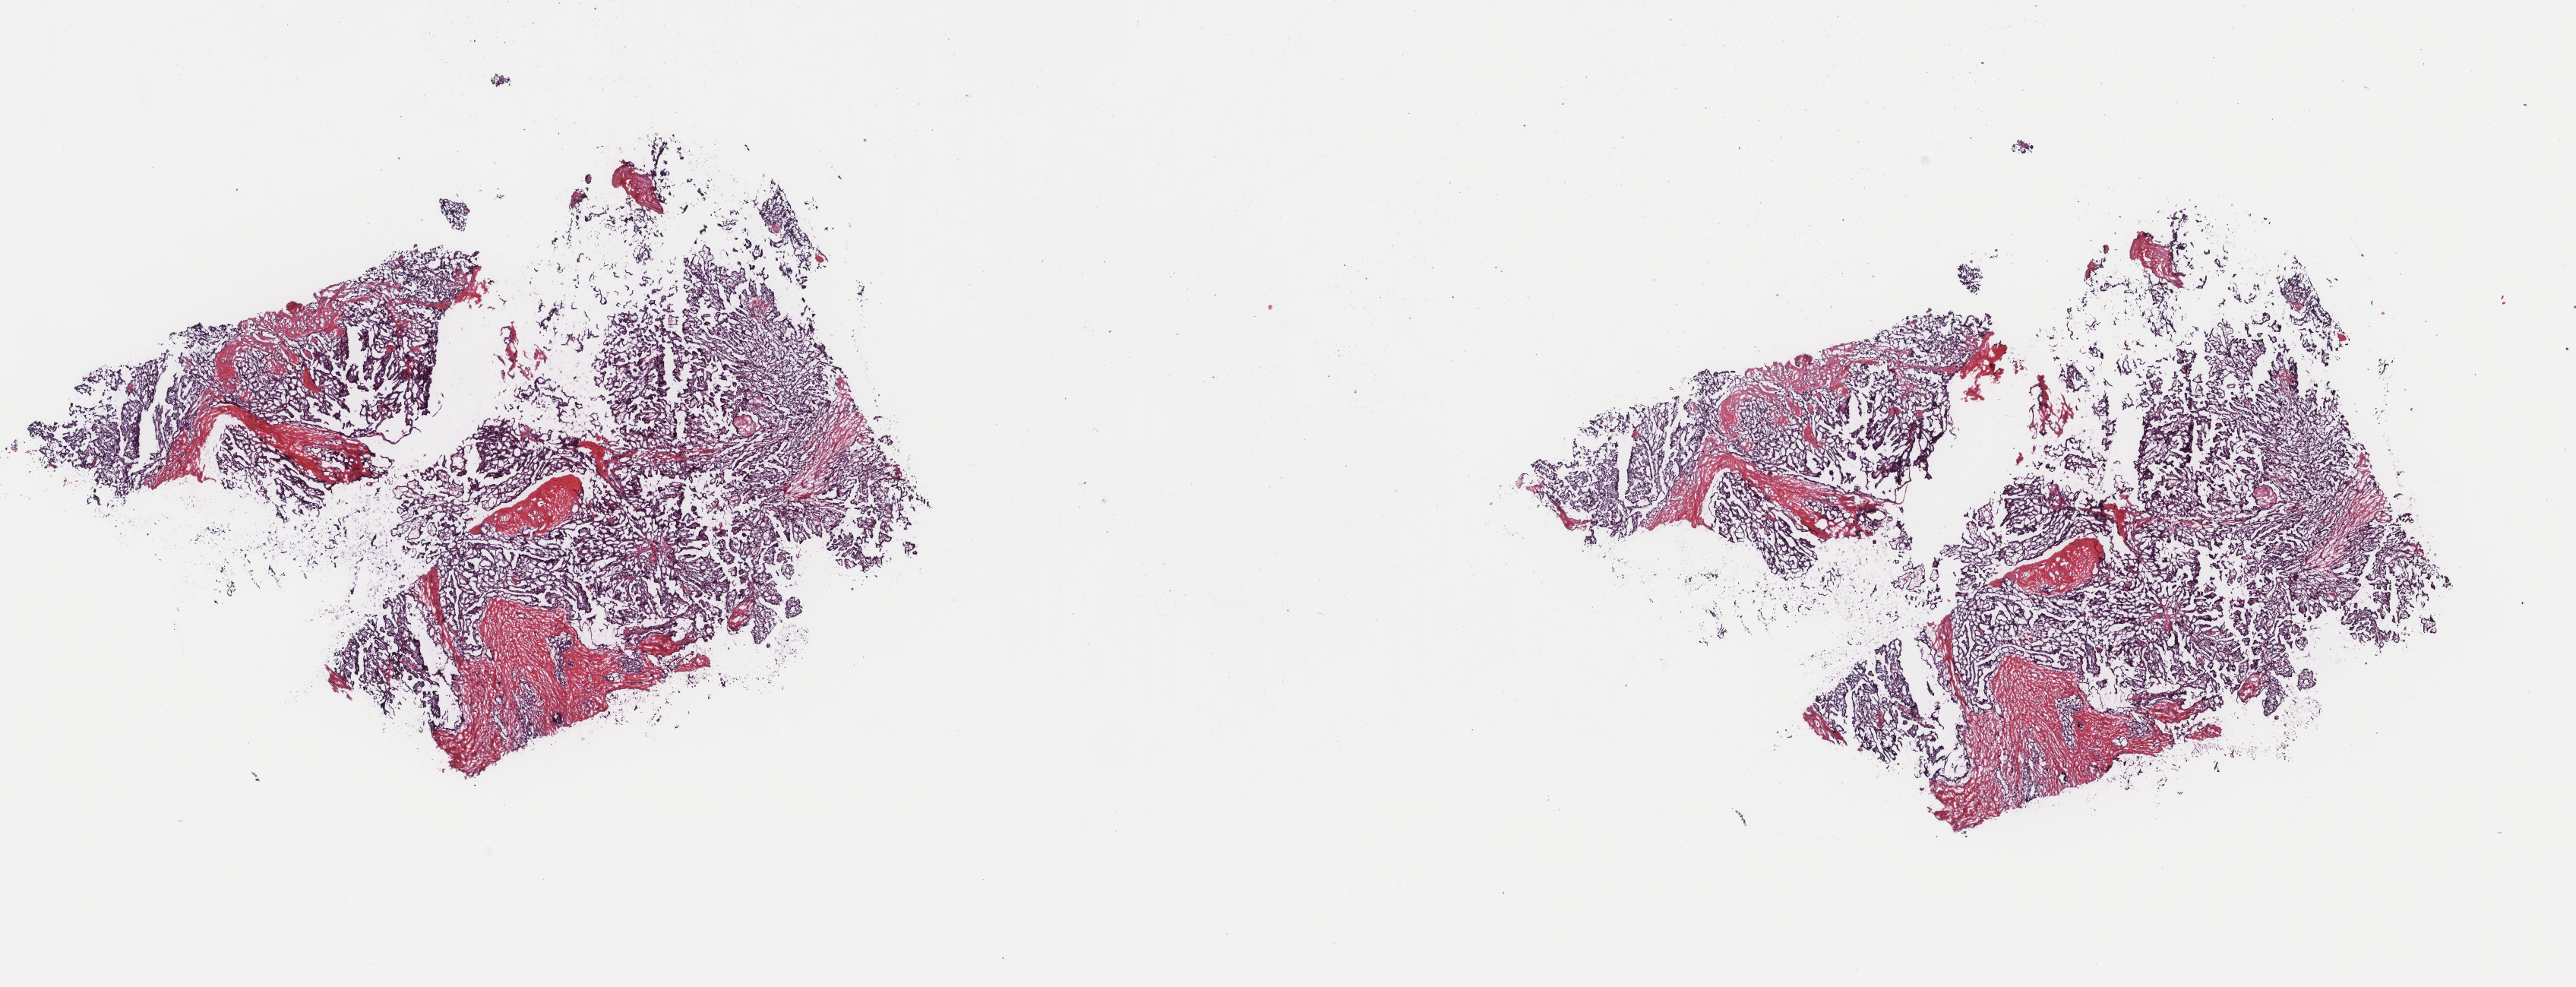
Hematoxylin and eosin (H&E) stained whole-slide image, low-resolution overview of the scanned area, about 26.9 x 10.3 mm (from a 40x scan); frozen section from the top of the tissue portion; sample: primary tumour, thyroid. Patient: female, age at initial diagnosis 39 years. Slide review estimates, as recorded: tumour cells 80%, tumour nuclei 80%, normal cells 0%, stromal cells 20%, necrosis 0%. Infiltration values recorded for this section: lymphocyte infiltration 2%, monocyte infiltration 0%, neutrophil infiltration 0%.
Lymph nodes positive (case pathology): 5 of 14 examined. AJCC pathologic stage: I (7th edition). Diagnosis: Papillary adenocarcinoma, NOS (thyroid gland). Laterality: bilateral.